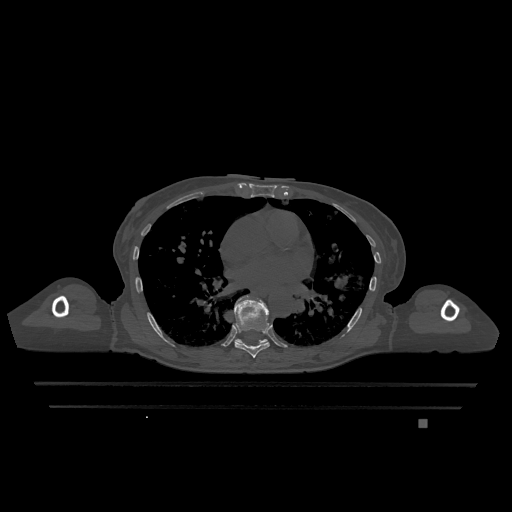
CT including the spine, one axial slice. Slice 727 of 1317 in the series (ordered by position). Bone window (W 1800 / L 400 HU). 0.5 mm slice thickness. 512 × 512 image matrix. Female patient, age 74 years. Case-level facts recorded for this patient, not image findings: primary cancer: lung; vertebrae with lytic lesions (as recorded): T1, T4, T5, T6, L4, L5.
Annotated regions visible in this slice (semi-automatic segmentation, software-assisted and operator-edited):
- T7 vertebra: bounding box [x1, y1, x2, y2] px = [234, 296, 270, 358]
- T9 vertebra: [235, 339, 268, 345]